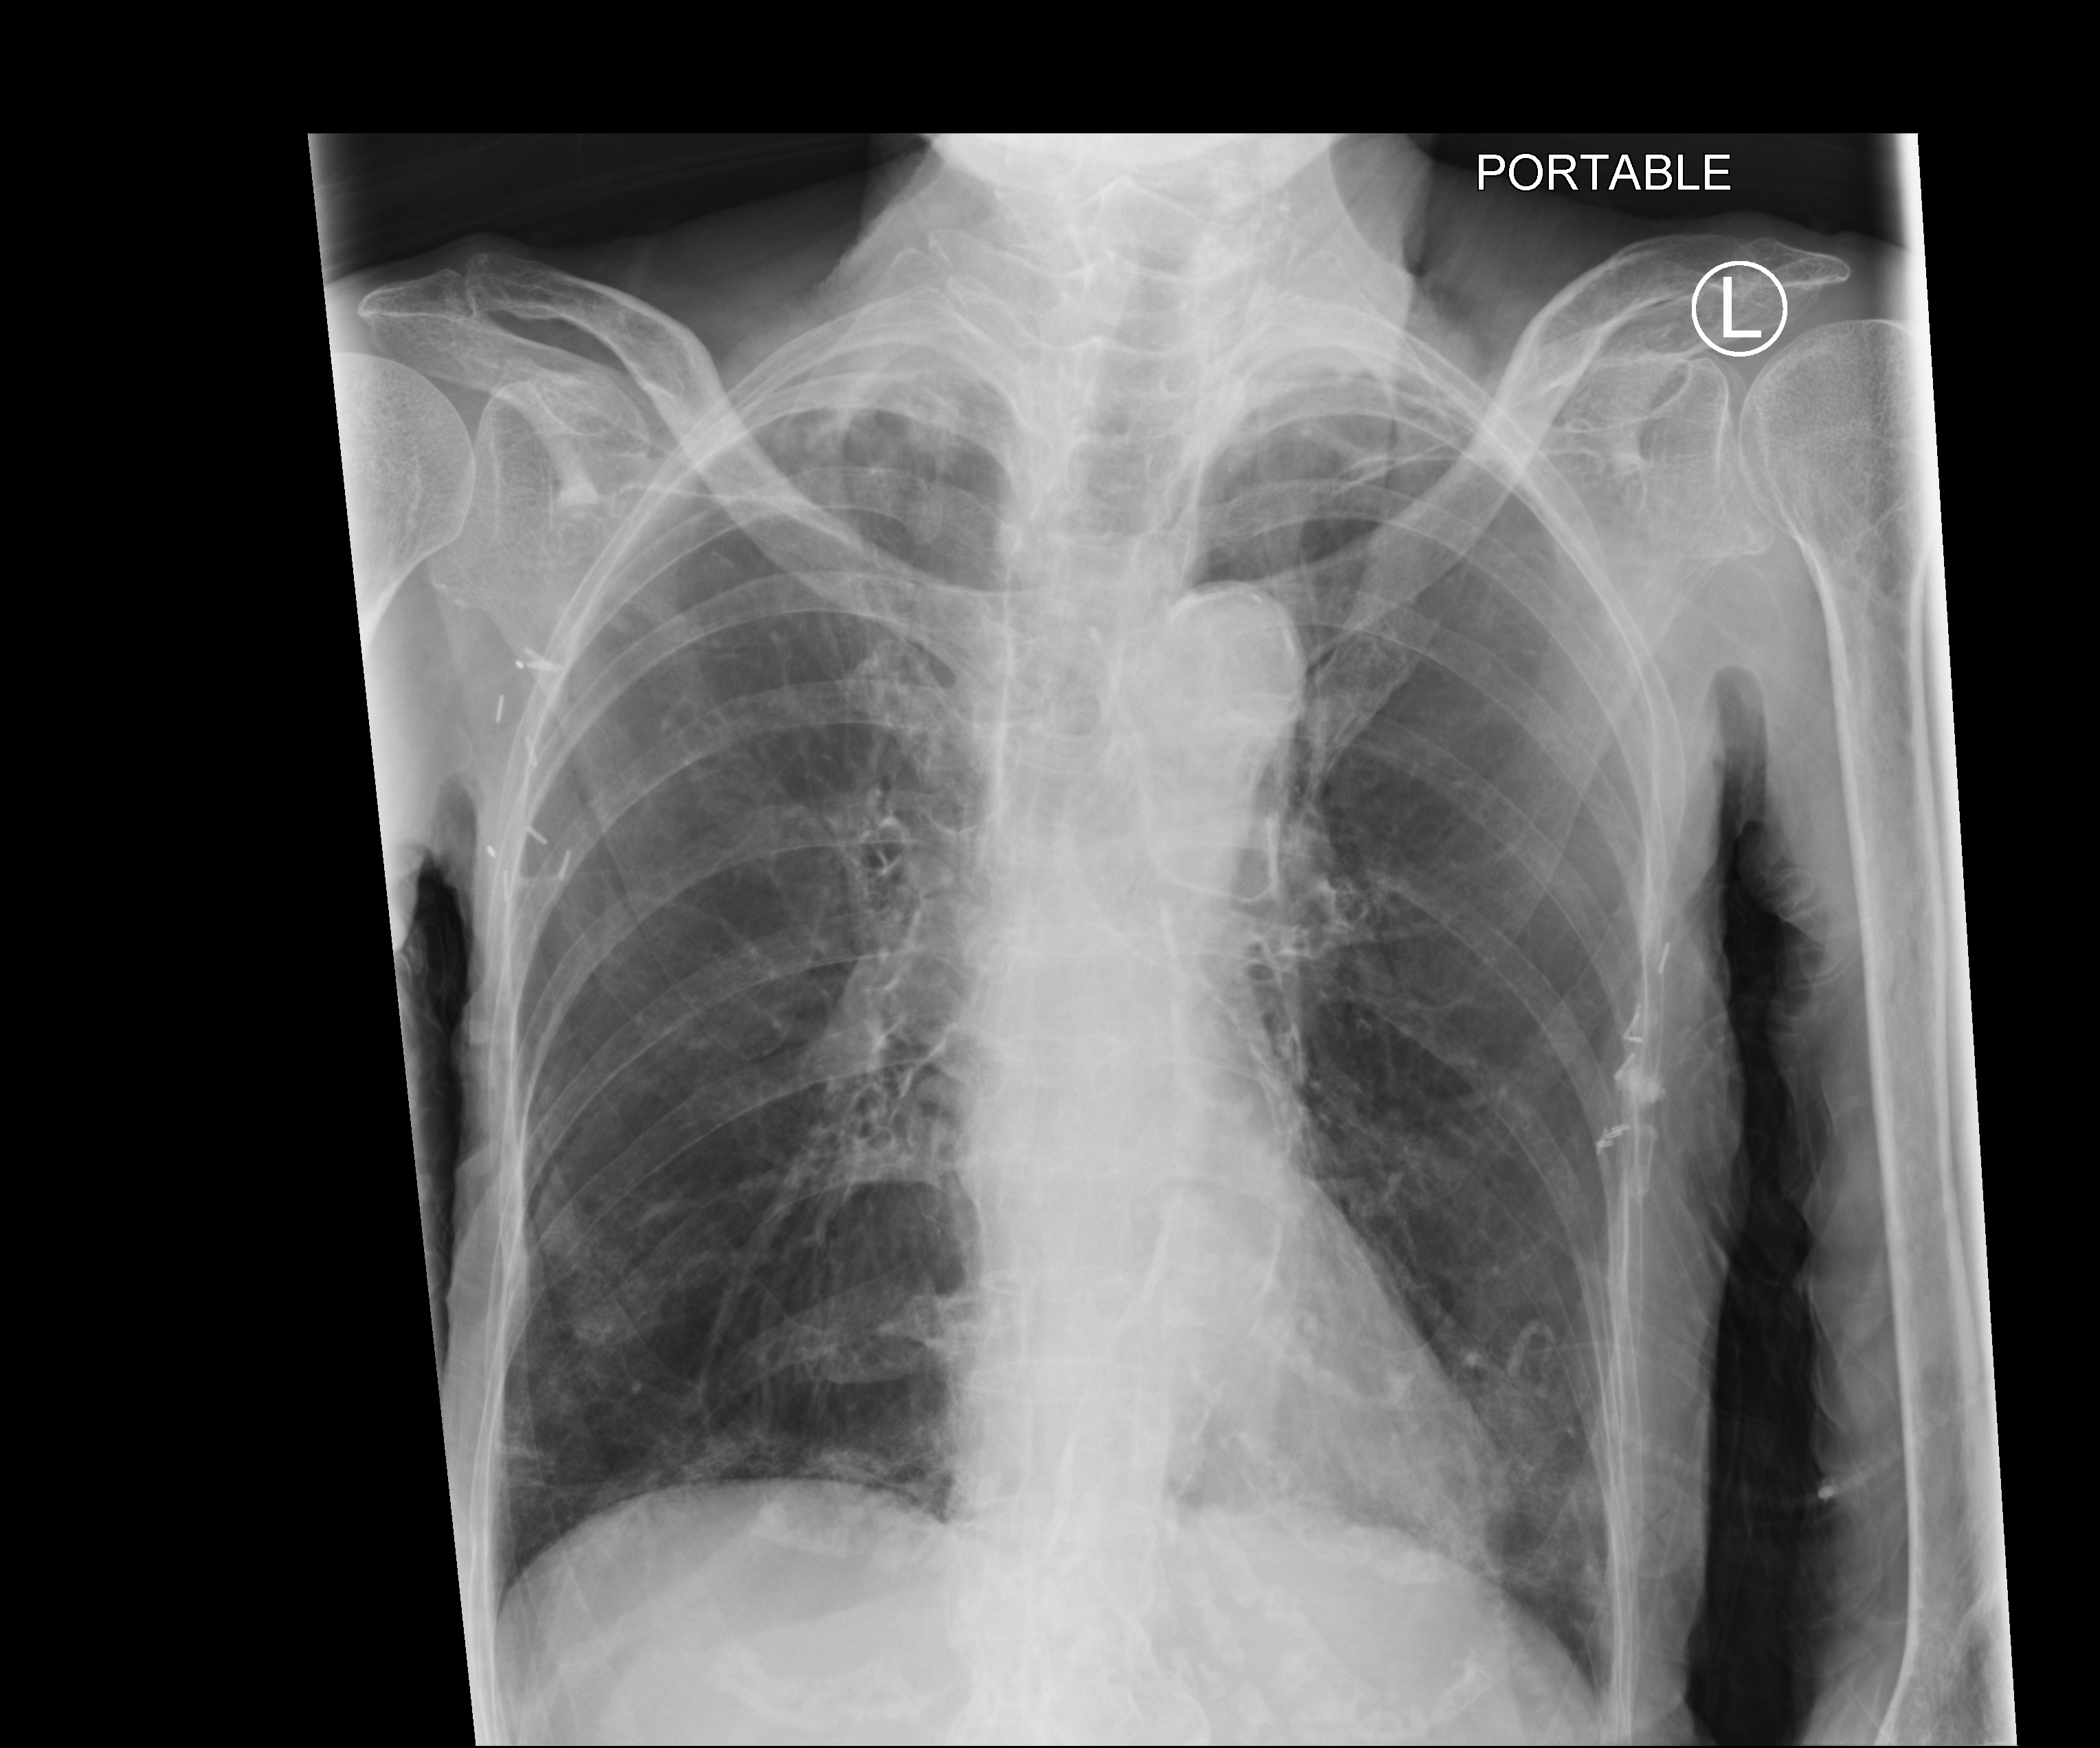
Bedside chest radiograph (computed radiography); anteroposterior (AP) projection. Female patient hospitalised with COVID-19, age 75–90 years.
Admission-level facts for this patient (not findings on this image; timing relative to this image not recorded): mechanically ventilated during this hospital stay: no; length of hospital stay: 5 days; admitted to intensive care during this hospital stay: no.